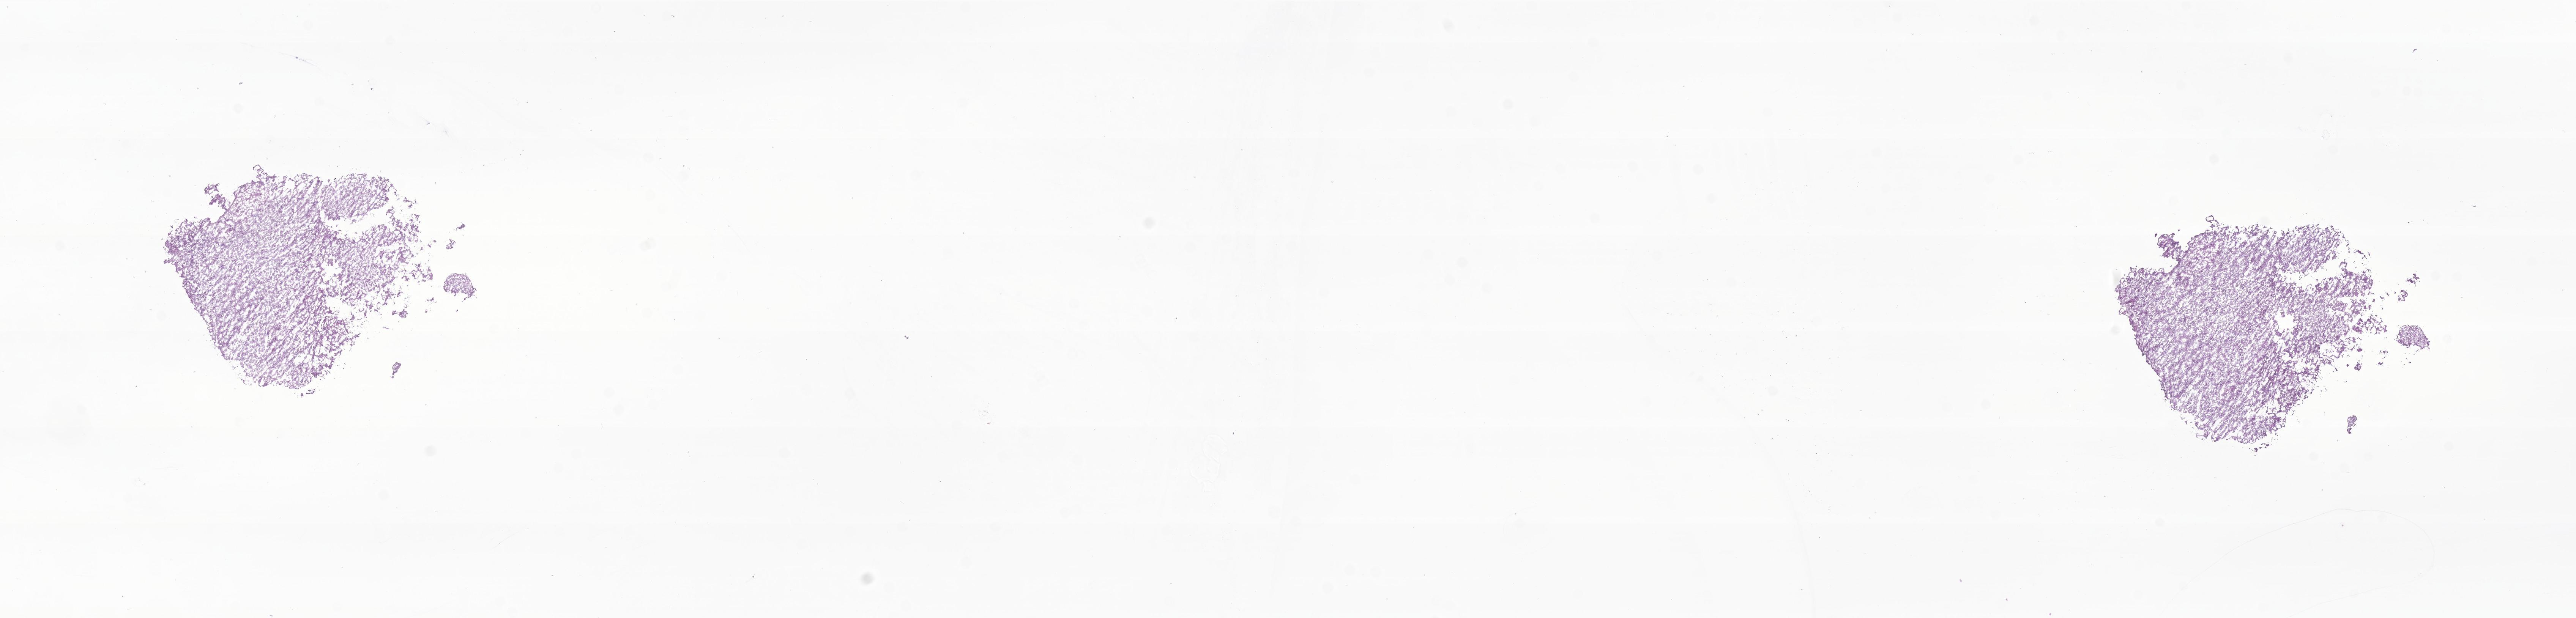
Hematoxylin and eosin (H&E) whole-slide image of tumor tissue from the brain — low-resolution overview of the scanned area, about 28.6 x 6.9 mm. Cryosection (OCT / tissue freezing medium). Patient female; age 221 months.
- diagnosis: Atypical meningioma